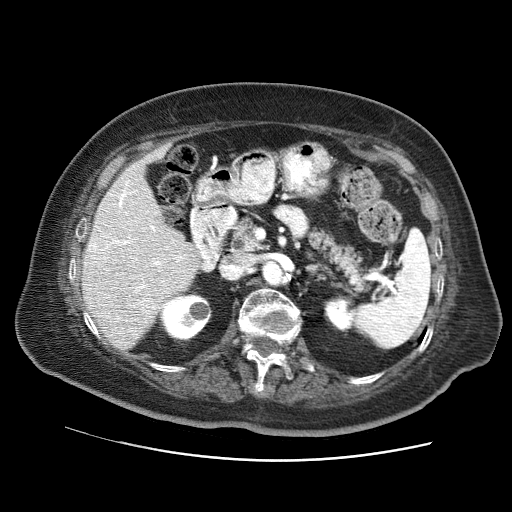
Contrast-enhanced abdominal CT (liver protocol), one axial slice. Position 33 of 73 along the scan axis. Soft-tissue window (W 400 / L 40 HU). 2.5 mm slice thickness. 512 × 512 image matrix, field of view 380 × 380 mm. From the clinical record (not read from this slice): diagnosis: hepatocellular carcinoma (patient treated with transarterial chemoembolisation; whether this scan precedes or follows treatment is not stated here); TNM stage (as recorded): Stage-I; Child-Pugh class: A; tumour nodularity: uninodular.
Annotated regions visible in this slice (semi-automatically segmented with operator editing):
- liver parenchyma outside the tumour (the mass and vessels are separate outlines, so this box may not span the whole liver): box from (x=82, y=145) to (x=200, y=350) px
- liver vessels: (x=90, y=181)–(x=182, y=331)